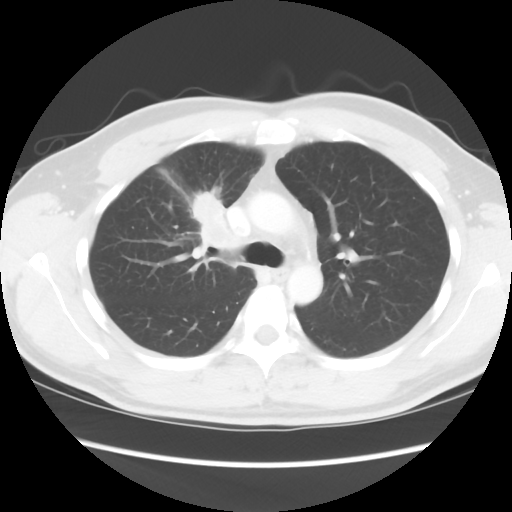
Chest CT, one axial slice; position 62 of 80 along the scan axis; reconstruction kernel STANDARD; 120 kVp; lung window (W 1500 / L -600 HU); 5 mm slice thickness; 512 × 512 image matrix. Male patient, age 35 years. Case-level facts recorded for this patient, not image findings: clinical TNM (as recorded): T1c N1 M1b.
Structures marked on this image (bounding box drawn by a radiologist):
- lung tumour (recorded histology: adenocarcinoma): box from (x=183, y=192) to (x=240, y=259) px